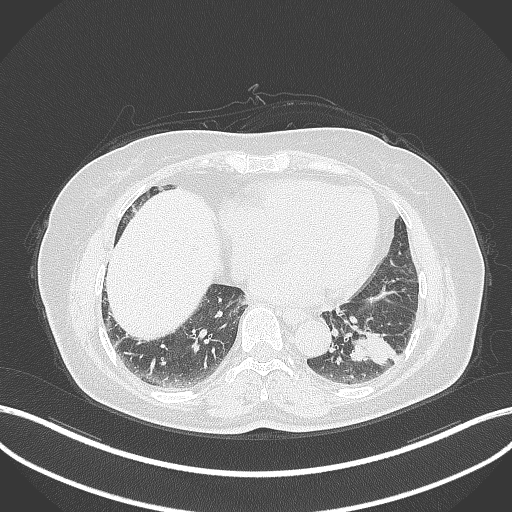
Chest CT, one axial slice. Position 132 of 311 along the scan axis. Reconstruction kernel B70f. 120 kVp. Lung window (W 1500 / L -600 HU). 1 mm slice thickness. 512 × 512 image matrix. Female patient, age 59 years. From the clinical record (not read from this slice): clinical TNM (as recorded): T2a N0 M0; histopathological grade: G2-3.
Annotated regions visible in this slice (rectangle marked by the reading radiologist):
- lung tumour (recorded histology: adenocarcinoma): bounding box [x1, y1, x2, y2] px = [344, 322, 397, 366]